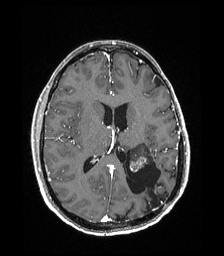
Brain MRI from a brain-tumour surgery series, one axial slice. Position 87 of 192 along the scan axis. T1-weighted post-contrast. 1 mm slice thickness. 224 × 256 image matrix. Case-level facts recorded for this patient, not image findings: histopathology: Low grade glioma; IDH mutation: no; tumour location: Left Parieto-Occipital Intraventricular.
Structures marked on this image (outlined manually by an expert reader):
- previous resection cavity: bounding box [x1, y1, x2, y2] px = [126, 152, 165, 207]
- tumour: [129, 143, 153, 172]